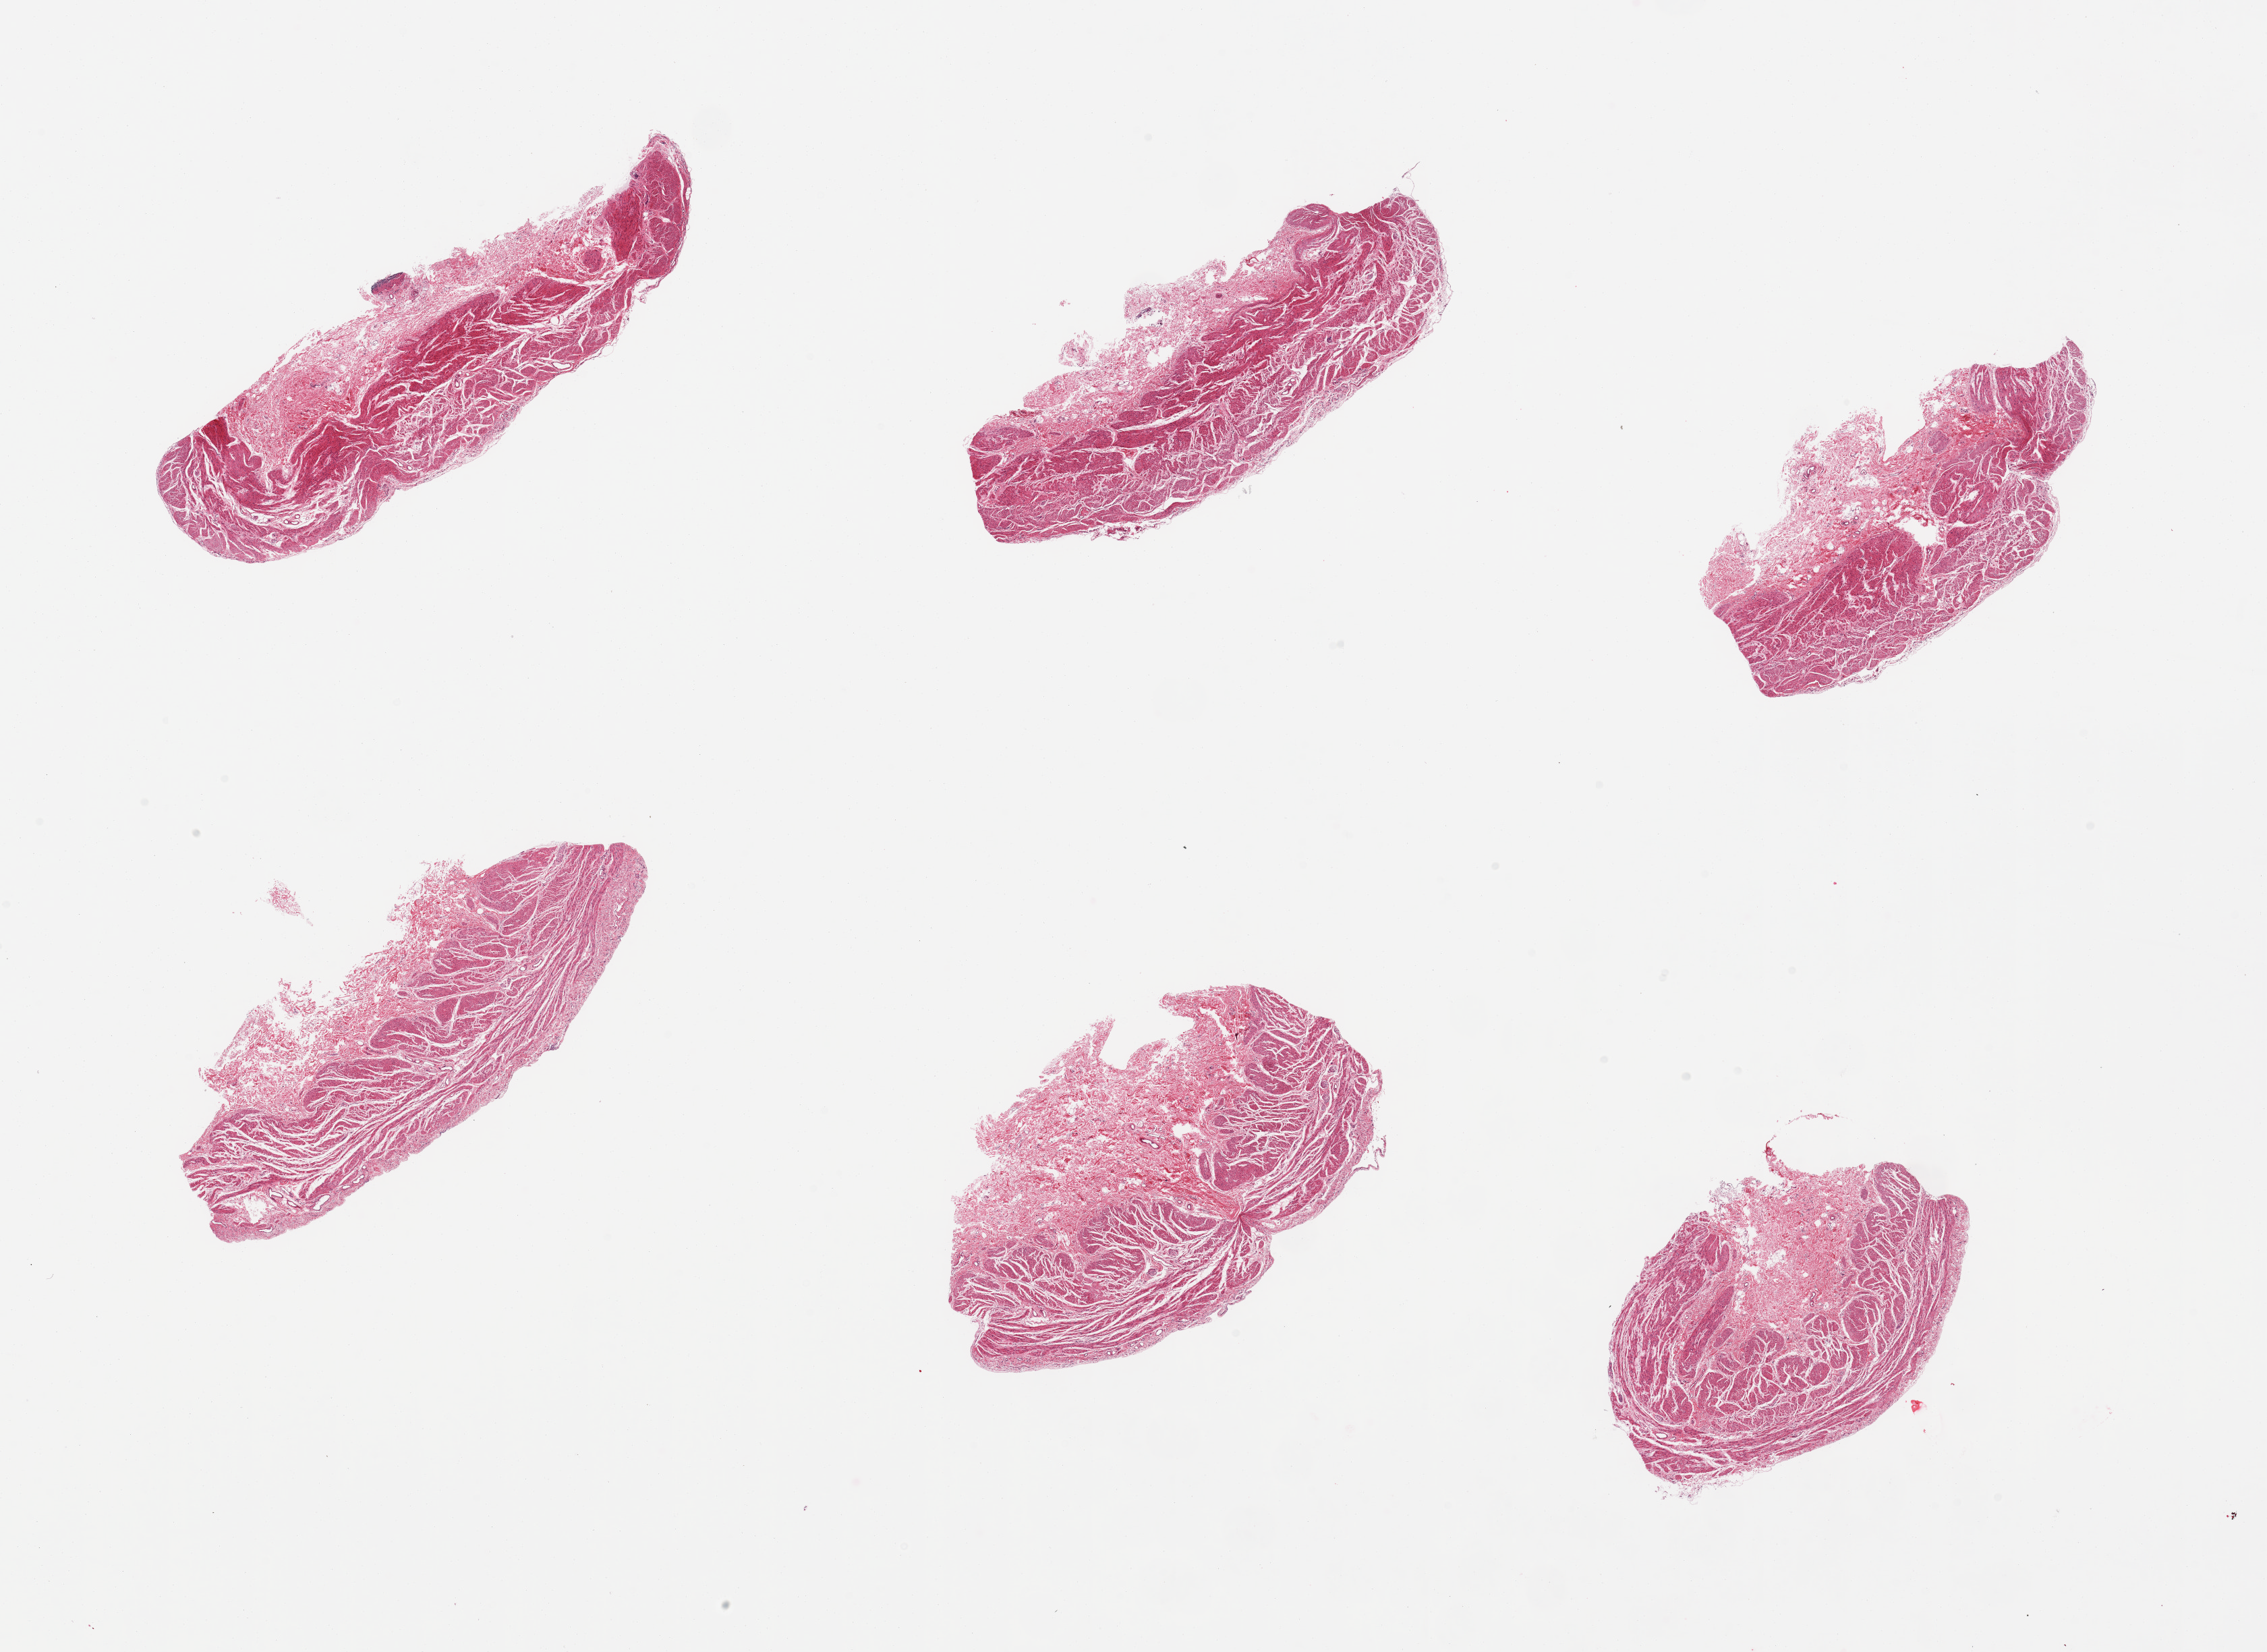
H&E whole-slide image, brightfield, shown as a low-resolution overview of the whole scanned area (about 26.6 x 19.4 mm); PAXgene-fixed paraffin-embedded (PFPE) section; section of stomach (target tissue); tissue donor sample.
Pathologist's review note for this sample: 6 pieces, muscularis only, mucosa sloughed.